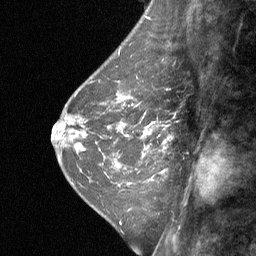
Breast MRI (dynamic contrast-enhanced), one sagittal slice. Position 22 of 64 along the scan axis. Dynamic contrast-enhanced study with each time point stored as its own series, time point 2 of 3 at this slice position (early post-contrast, ordered by acquisition time). 1.5 T. TE 4.8 ms, TR 27 ms. 2 mm slice thickness. 256 × 256 image matrix, field of view 180 × 180 mm. Patient: female, 42 years. Case-level facts recorded for this patient, not image findings: setting: breast cancer imaged before/during neoadjuvant chemotherapy; receptor status: triple-negative.
Annotated regions visible in this slice (semi-automatically segmented with operator editing):
- analysis volume of interest (the breast-tissue region the enhancement analysis was run in; not a lesion): bounding box (x1, y1, x2, y2) in pixels: (124, 94, 171, 161)
- tumour enhancement mask (voxels above the 90 % enhancement threshold inside the analysis volume of interest): (142, 125, 169, 143)